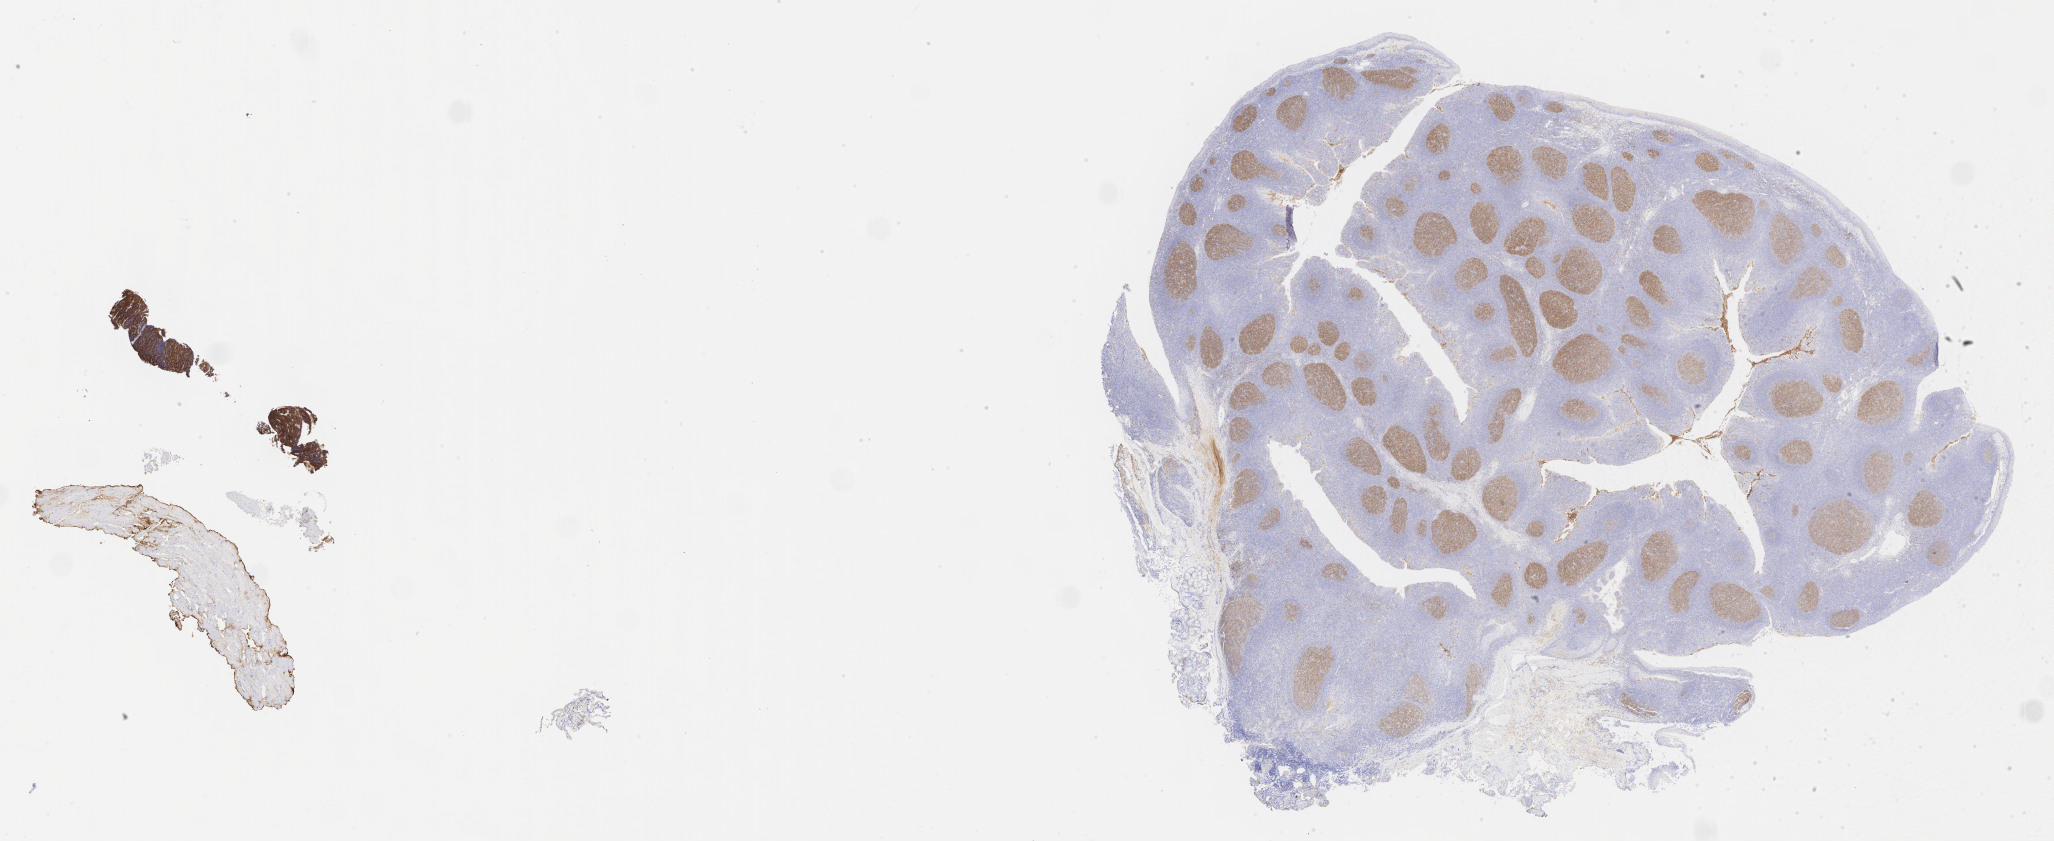
IHC for CD10, whole-slide image, whole scanned area (about 33.2 x 13.6 mm) shown as a low-resolution overview. Tumor tissue. Site: liver. Male patient.
Histologic diagnosis: Burkitt lymphoma, NOS.